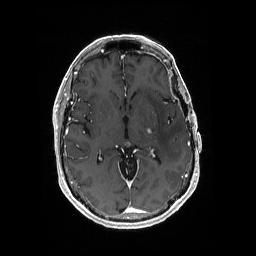
Brain MRI from a brain-tumour surgery series, one axial slice. Slice 103 of 176 in the series (ordered by position). T1-weighted post-contrast. 1 mm slice thickness. 256 × 256 image matrix, field of view 256 × 256 mm. From the clinical record (not read from this slice): histopathology: Glioblastoma; WHO grade: 4; IDH mutation: no.
Outlined on this slice (manually delineated by an expert):
- tumour: bounding box [x1, y1, x2, y2] px = [147, 129, 152, 134]